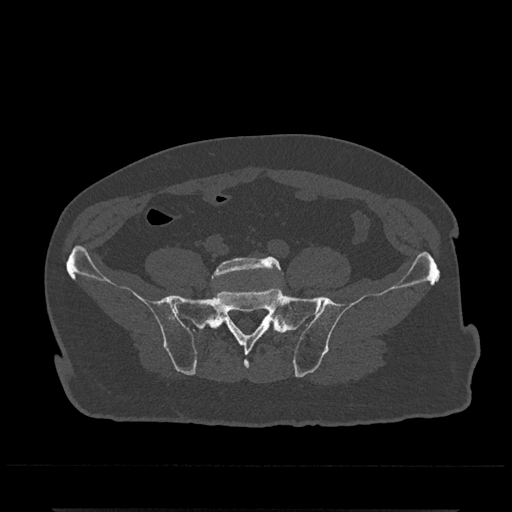
CT including the spine, one axial slice; position 41 of 797 along the scan axis; reconstruction kernel Br40s/3; bone window (W 1800 / L 400 HU); 0.5 mm slice thickness; 512 × 512 image matrix, field of view 393 × 393 mm. Male patient, age 67 years. From the clinical record (not read from this slice): primary cancer: prostate.
Annotated regions visible in this slice (semi-automatically segmented with operator editing):
- L5 vertebra: bounding box (x1, y1, x2, y2) in pixels: (212, 256, 284, 292)